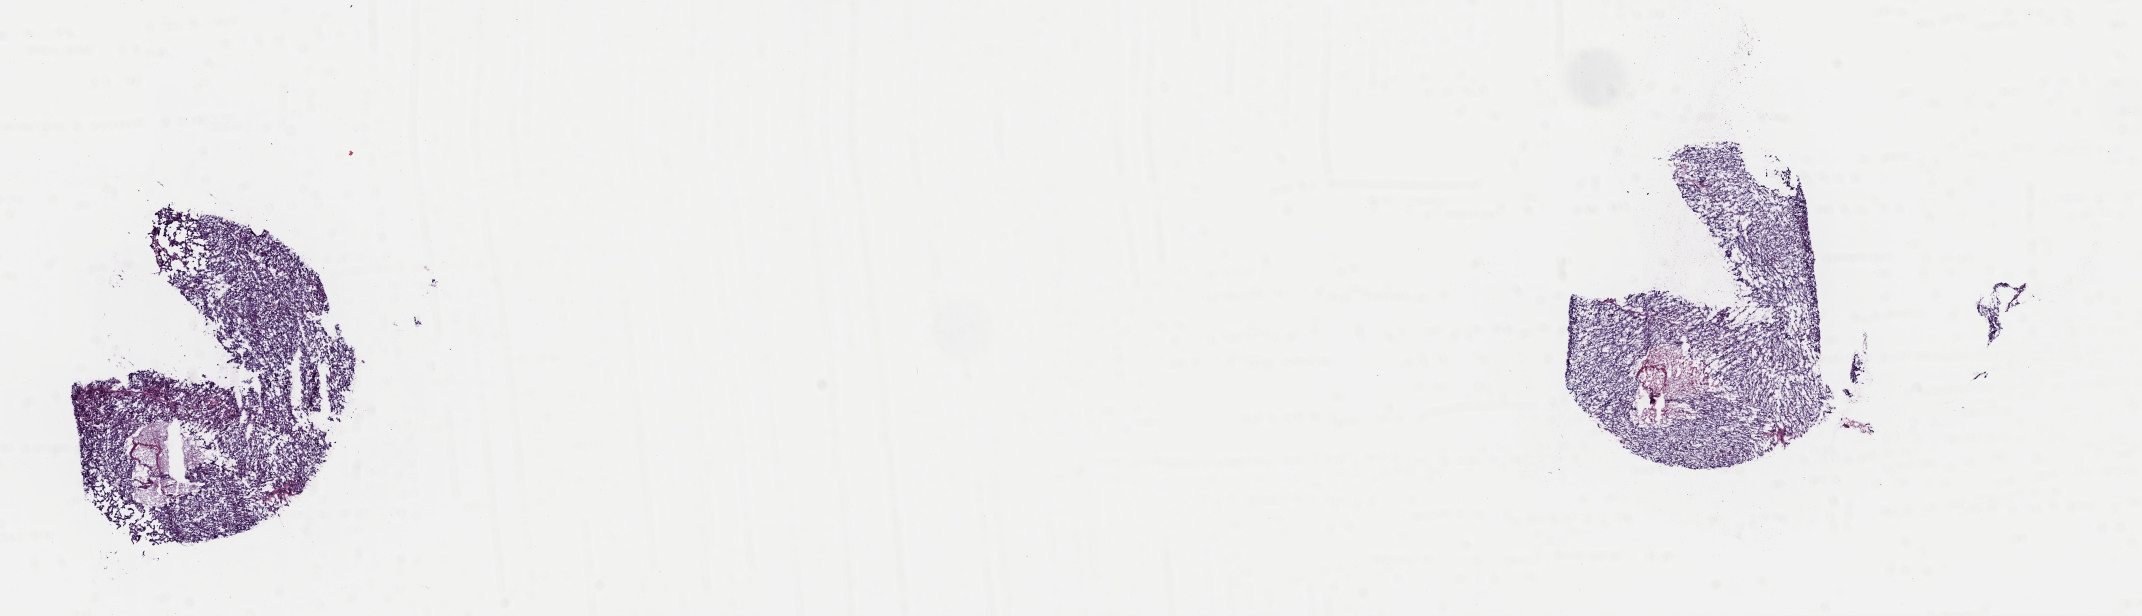
Whole-slide histology image, H&E-stained — shown as a low-resolution overview of the whole scanned area (about 16.9 x 4.9 mm, acquisition: 40x scan). Frozen section. Adrenal gland, primary tumour sample. Patient: female, age at initial diagnosis 42 years. Composition of this section per pathologist review: tumour cells 80%, tumour nuclei 90%.
Pathologic diagnosis: Pheochromocytoma, malignant.